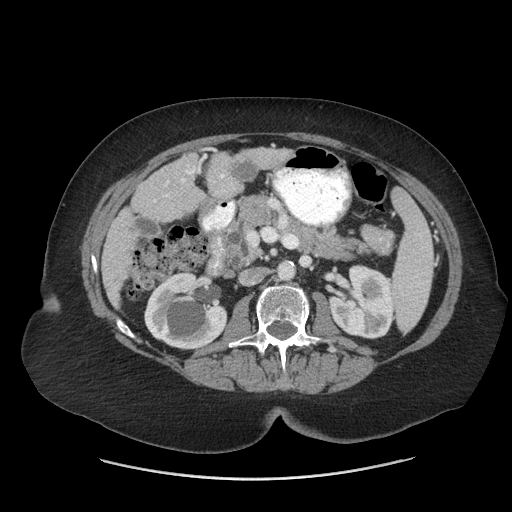
Contrast-enhanced abdominal CT (liver protocol), one axial slice; reconstruction kernel STANDARD; soft-tissue window (W 400 / L 40 HU); 2.5 mm slice thickness; 512 × 512 image matrix. From the clinical record (not read from this slice): diagnosis: hepatocellular carcinoma (patient treated with transarterial chemoembolisation; whether this scan precedes or follows treatment is not stated here); TNM stage (as recorded): Stage-IIIB; Child-Pugh class: A; tumour differentiation: moderately differentiated.
Structures marked on this image (semi-automatic segmentation, software-assisted and operator-edited):
- liver parenchyma outside the tumour (the mass and vessels are separate outlines, so this box may not span the whole liver): box from (x=102, y=147) to (x=291, y=306) px
- liver vessels: (x=154, y=167)–(x=224, y=202)